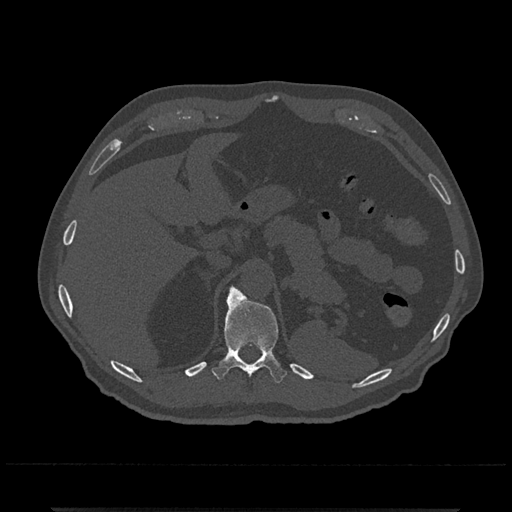
CT including the spine, one axial slice; slice 494 of 797 in the series (ordered by position); 120 kVp; bone window (W 1800 / L 400 HU); 0.5 mm slice thickness; 512 × 512 image matrix, field of view 393 × 393 mm. Male patient, age 67 years. Case-level facts recorded for this patient, not image findings: primary cancer: prostate.
Outlined on this slice (semi-automatic segmentation, software-assisted and operator-edited):
- T11 vertebra: box from (x=212, y=285) to (x=287, y=383) px